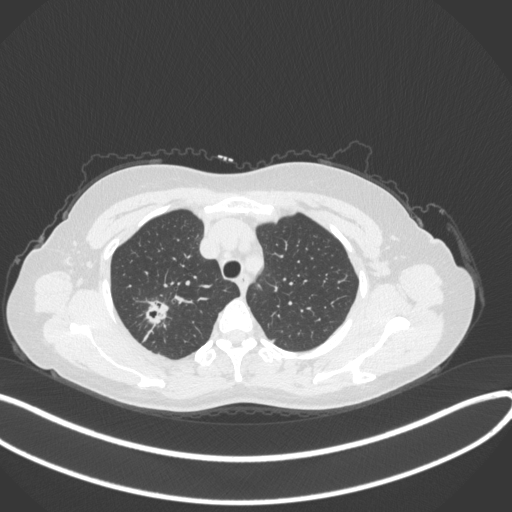
Chest CT, one axial slice. Position 291 of 342 along the scan axis. Reconstruction kernel B31f. Lung window (W 1500 / L -600 HU). 1 mm slice thickness. 512 × 512 image matrix, field of view 400 × 400 mm. Female patient, age 50 years. From the clinical record (not read from this slice): clinical TNM (as recorded): T1c N0 M0; histopathological grade: G2-3.
Annotated regions visible in this slice (rectangle marked by the reading radiologist):
- lung tumour (recorded histology: adenocarcinoma): bounding box <139,296,169,328> (left, top, right, bottom; pixels)